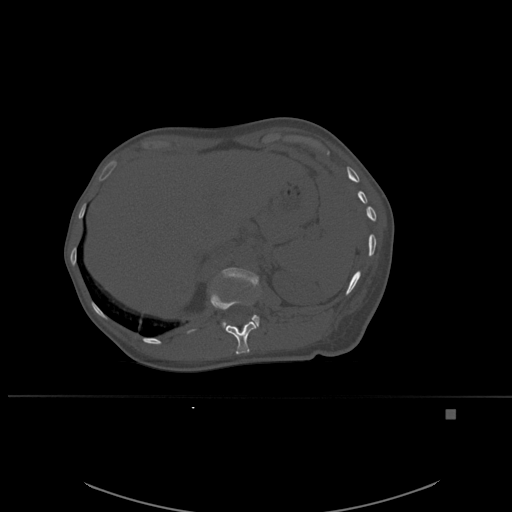
CT including the spine, one axial slice. Slice 272 of 537 in the series (ordered by position). Bone window (W 1800 / L 400 HU). 512 × 512 image matrix. Patient: female, 45 years. Case-level facts recorded for this patient, not image findings: primary cancer: lung.
Structures marked on this image (semi-automatically segmented with operator editing):
- L1 vertebra: box from (x=214, y=267) to (x=260, y=330) px
- T12 vertebra: (x=210, y=278)–(x=257, y=354)